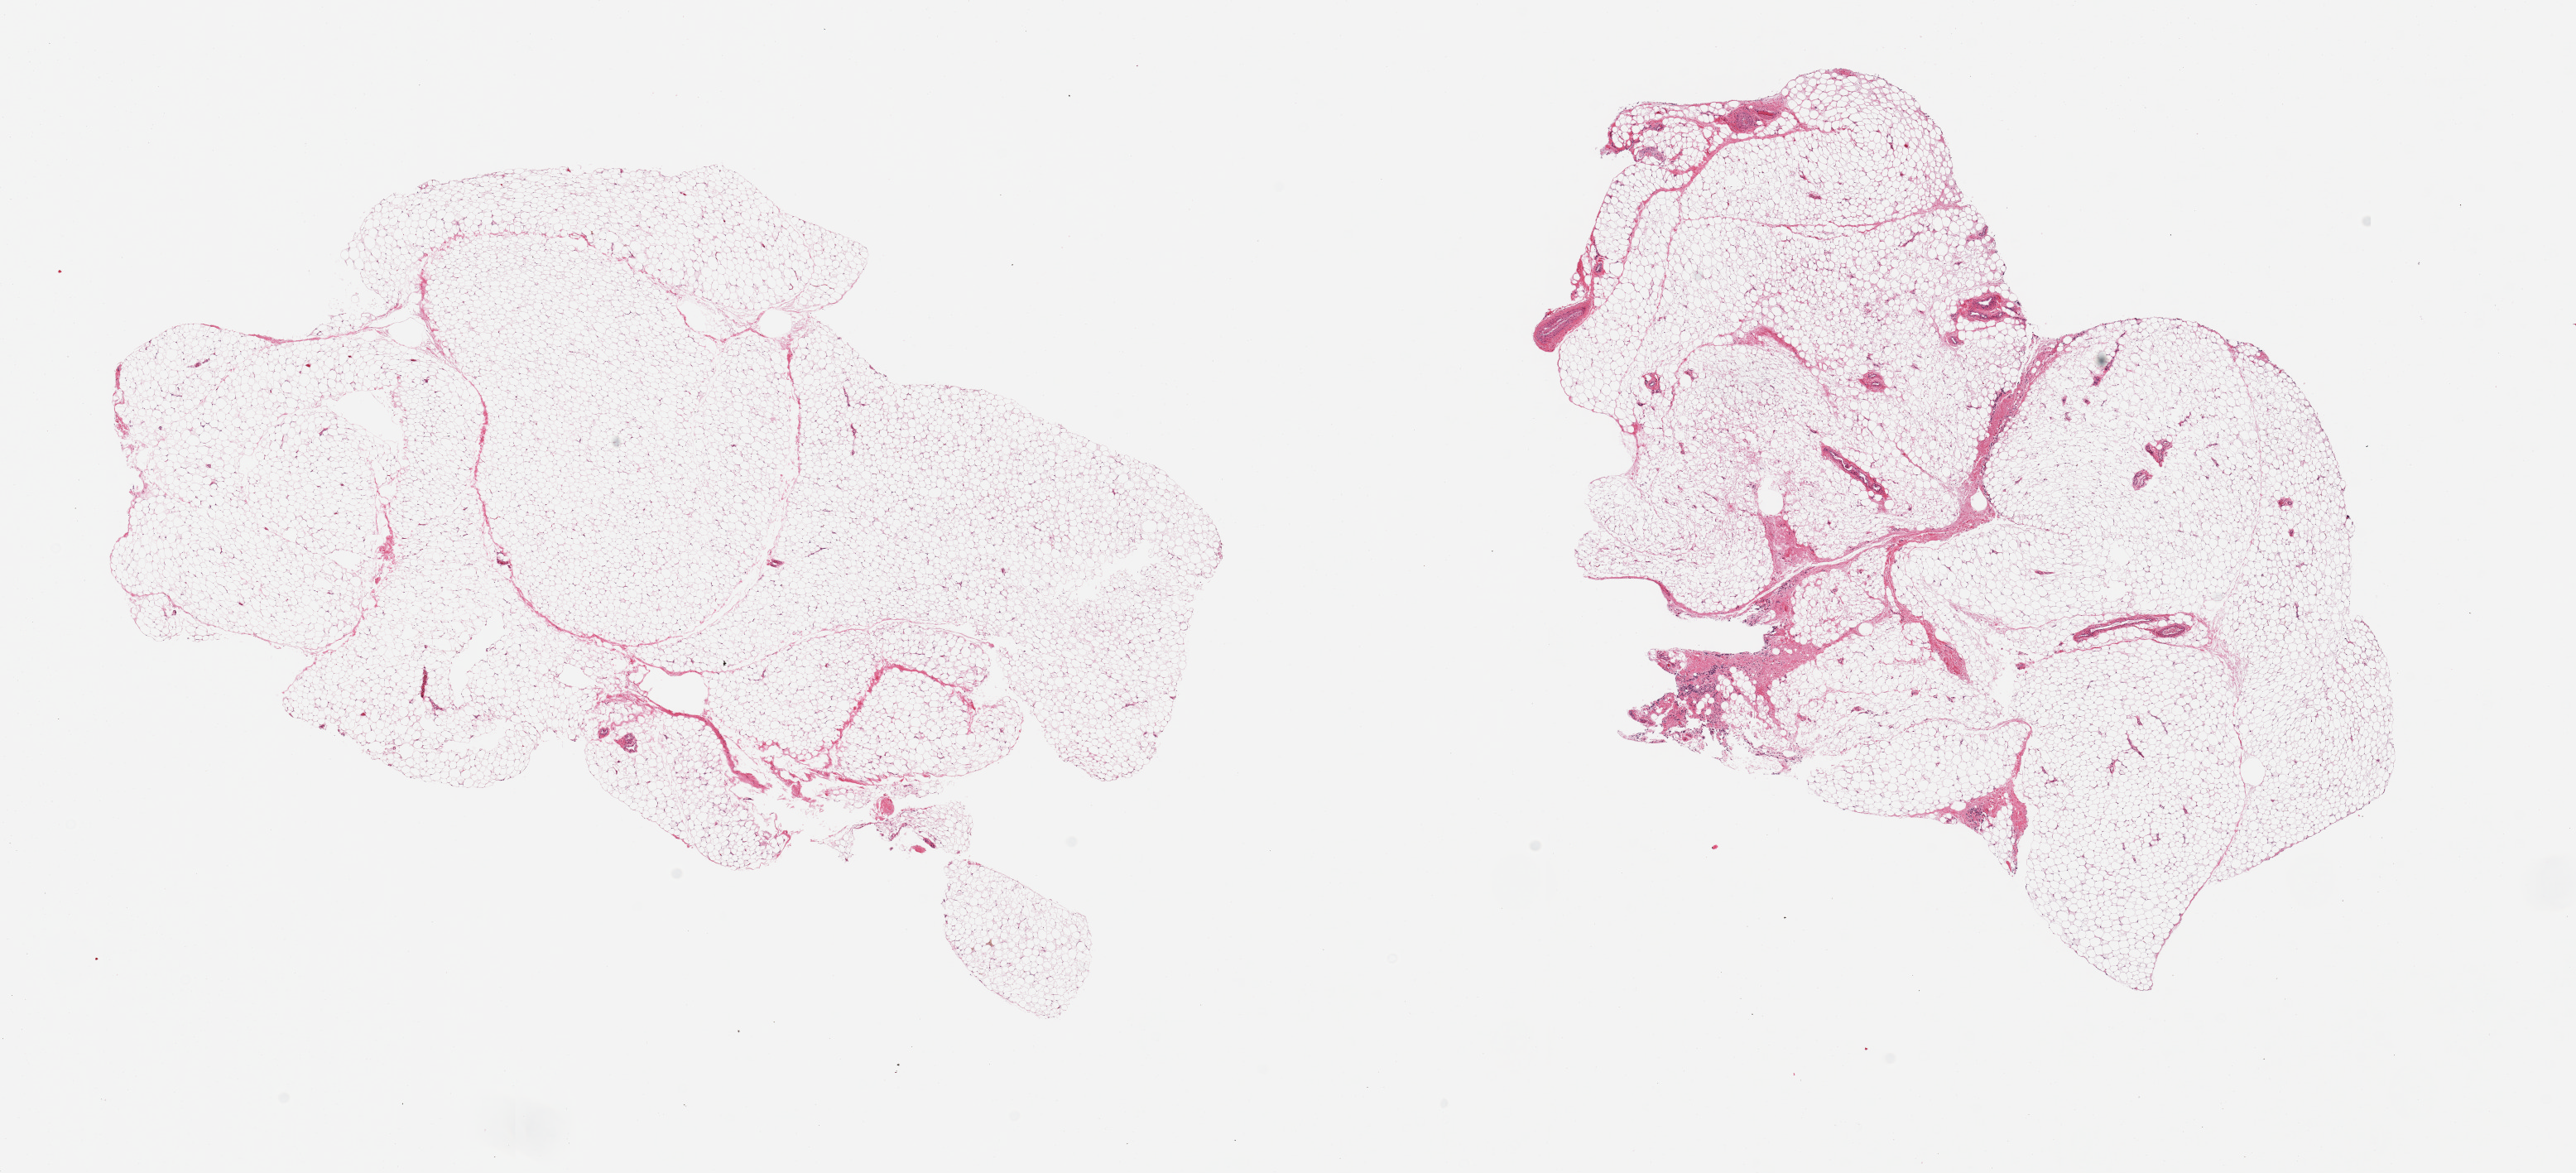
Digitized H&E-stained section — low-resolution overview of the scanned area, about 24.6 x 11.2 mm. PAXgene-fixed, paraffin-embedded tissue. Section of omentum (target tissue). Tissue donor sample. Donor: male.
Pathologist's review note for this sample: 2 pieces, ~5% interstitial fascia.